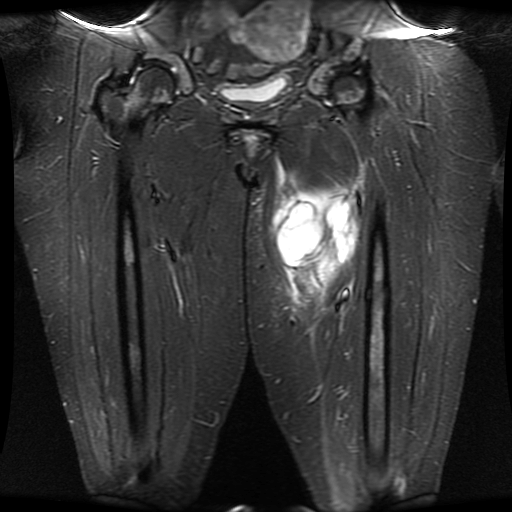
MRI of an extremity soft-tissue mass, one coronal slice; position 12 of 30 along the scan axis; STIR; 5 mm slice thickness; 512 × 512 image matrix, field of view 460 × 460 mm. Female patient. From the clinical record (not read from this slice): histological type: myxofibrosarcoma; grade: intermediate; site of the primary tumour: left thigh.
Annotated regions visible in this slice (outlined manually by an expert reader):
- gross tumour volume including surrounding oedema: bounding box (x1, y1, x2, y2) in pixels: (270, 158, 364, 316)
- gross tumour volume (mass): (273, 192, 359, 269)